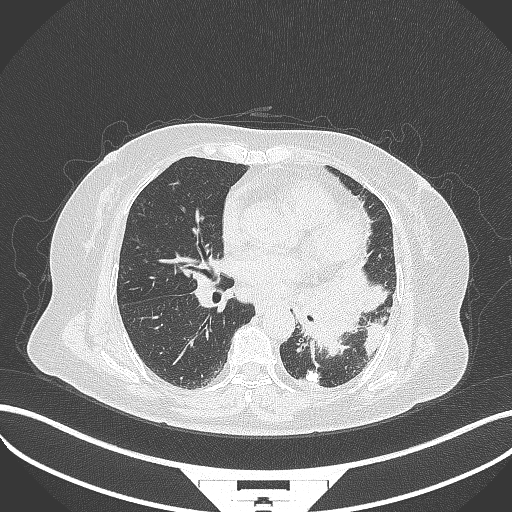
Chest CT, one axial slice. Position 167 of 322 along the scan axis. 120 kVp. Lung window (W 1500 / L -600 HU). 1 mm slice thickness. 512 × 512 image matrix, field of view 400 × 400 mm. Patient: female, 69 years. Case-level facts recorded for this patient, not image findings: clinical TNM (as recorded): T2b N3 M1.
Outlined on this slice (bounding box drawn by a radiologist):
- lung tumour (recorded histology: adenocarcinoma): bounding box <306,264,391,357> (left, top, right, bottom; pixels)